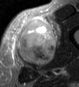
MRI of an extremity soft-tissue mass, one axial slice; position 23 of 45 along the scan axis; STIR; MR volume resampled by the dataset authors to the PET/CT grid (not the native acquisition matrix); 79 × 87 image matrix, field of view 77 × 85 mm. Male patient. From the clinical record (not read from this slice): histological type: pleiomorphic leiomyosarcoma; grade: high; site of the primary tumour: left thigh.
Annotated regions visible in this slice (expert contour drawn on MRI and transferred to this co-registered scan by the dataset authors):
- gross tumour volume including surrounding oedema: box from (x=15, y=16) to (x=60, y=67) px
- gross tumour volume (mass): (x=15, y=16)–(x=55, y=65)